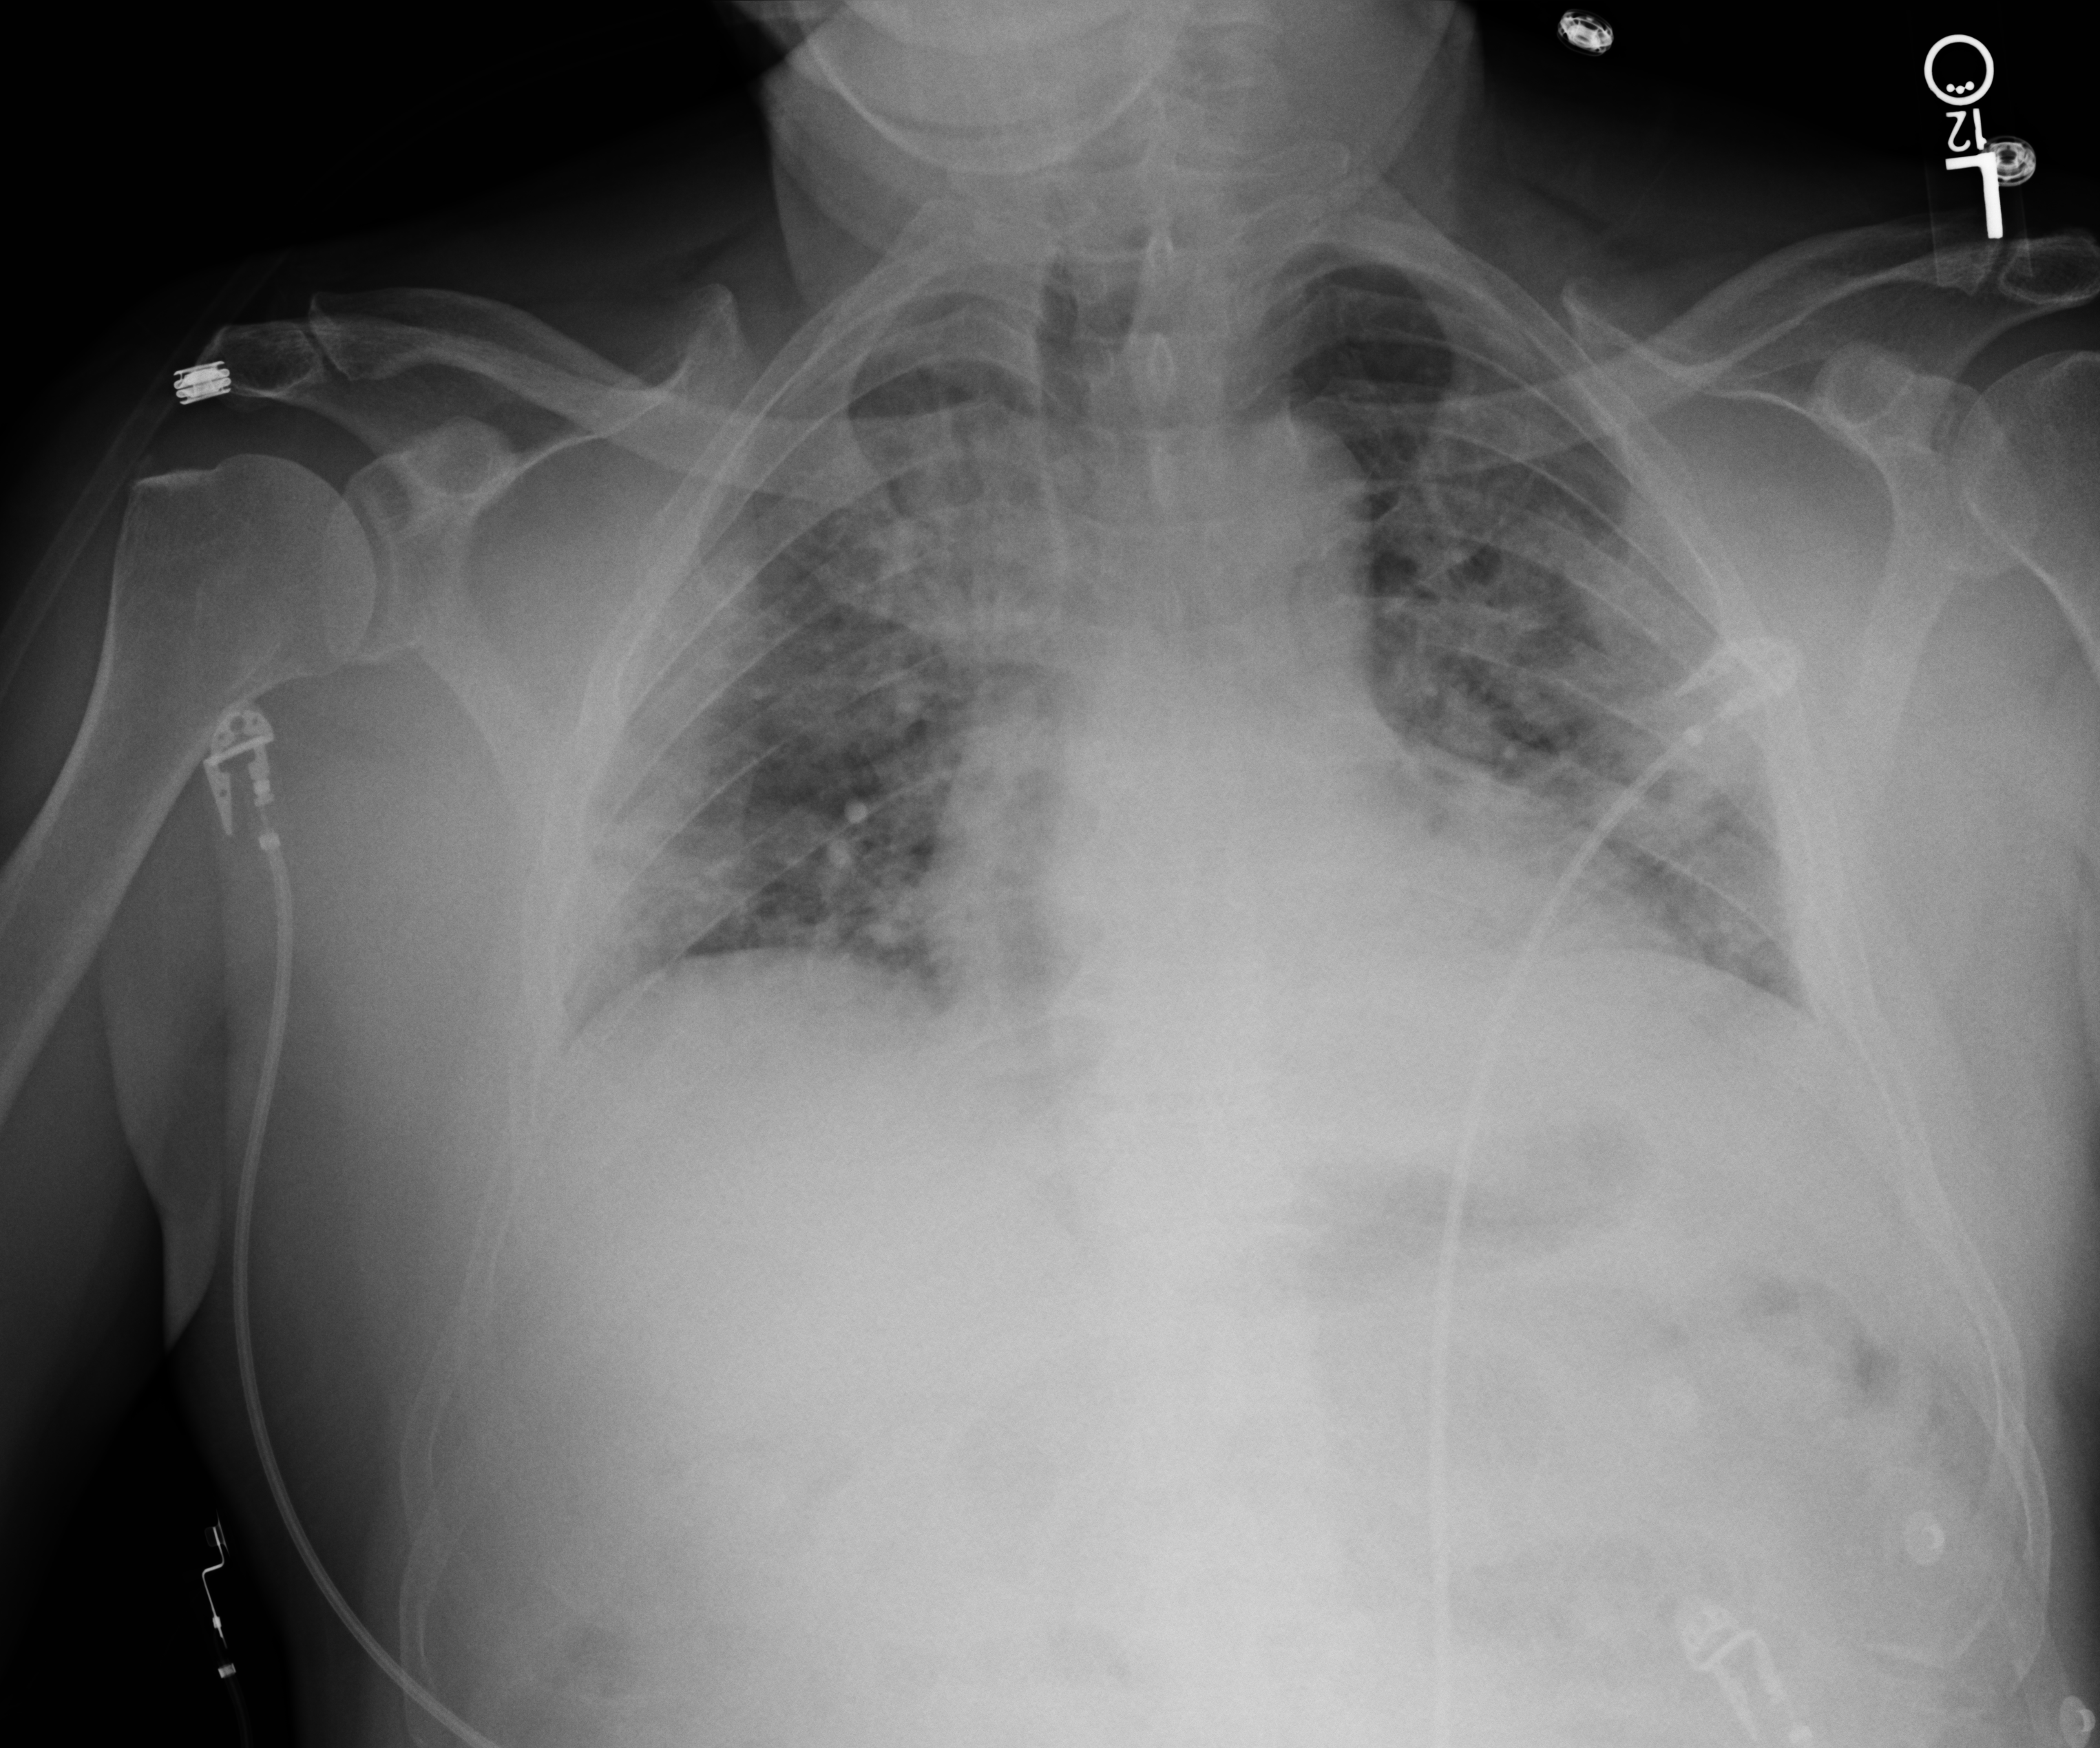
Portable chest radiograph; anteroposterior (AP) projection. Patient hospitalised with COVID-19; male, aged 60–74 years.
Hospital-stay facts (about this admission, not read from this image; timing relative to this image not recorded):
- mechanically ventilated during this hospital stay: no
- admitted to intensive care during this hospital stay: no